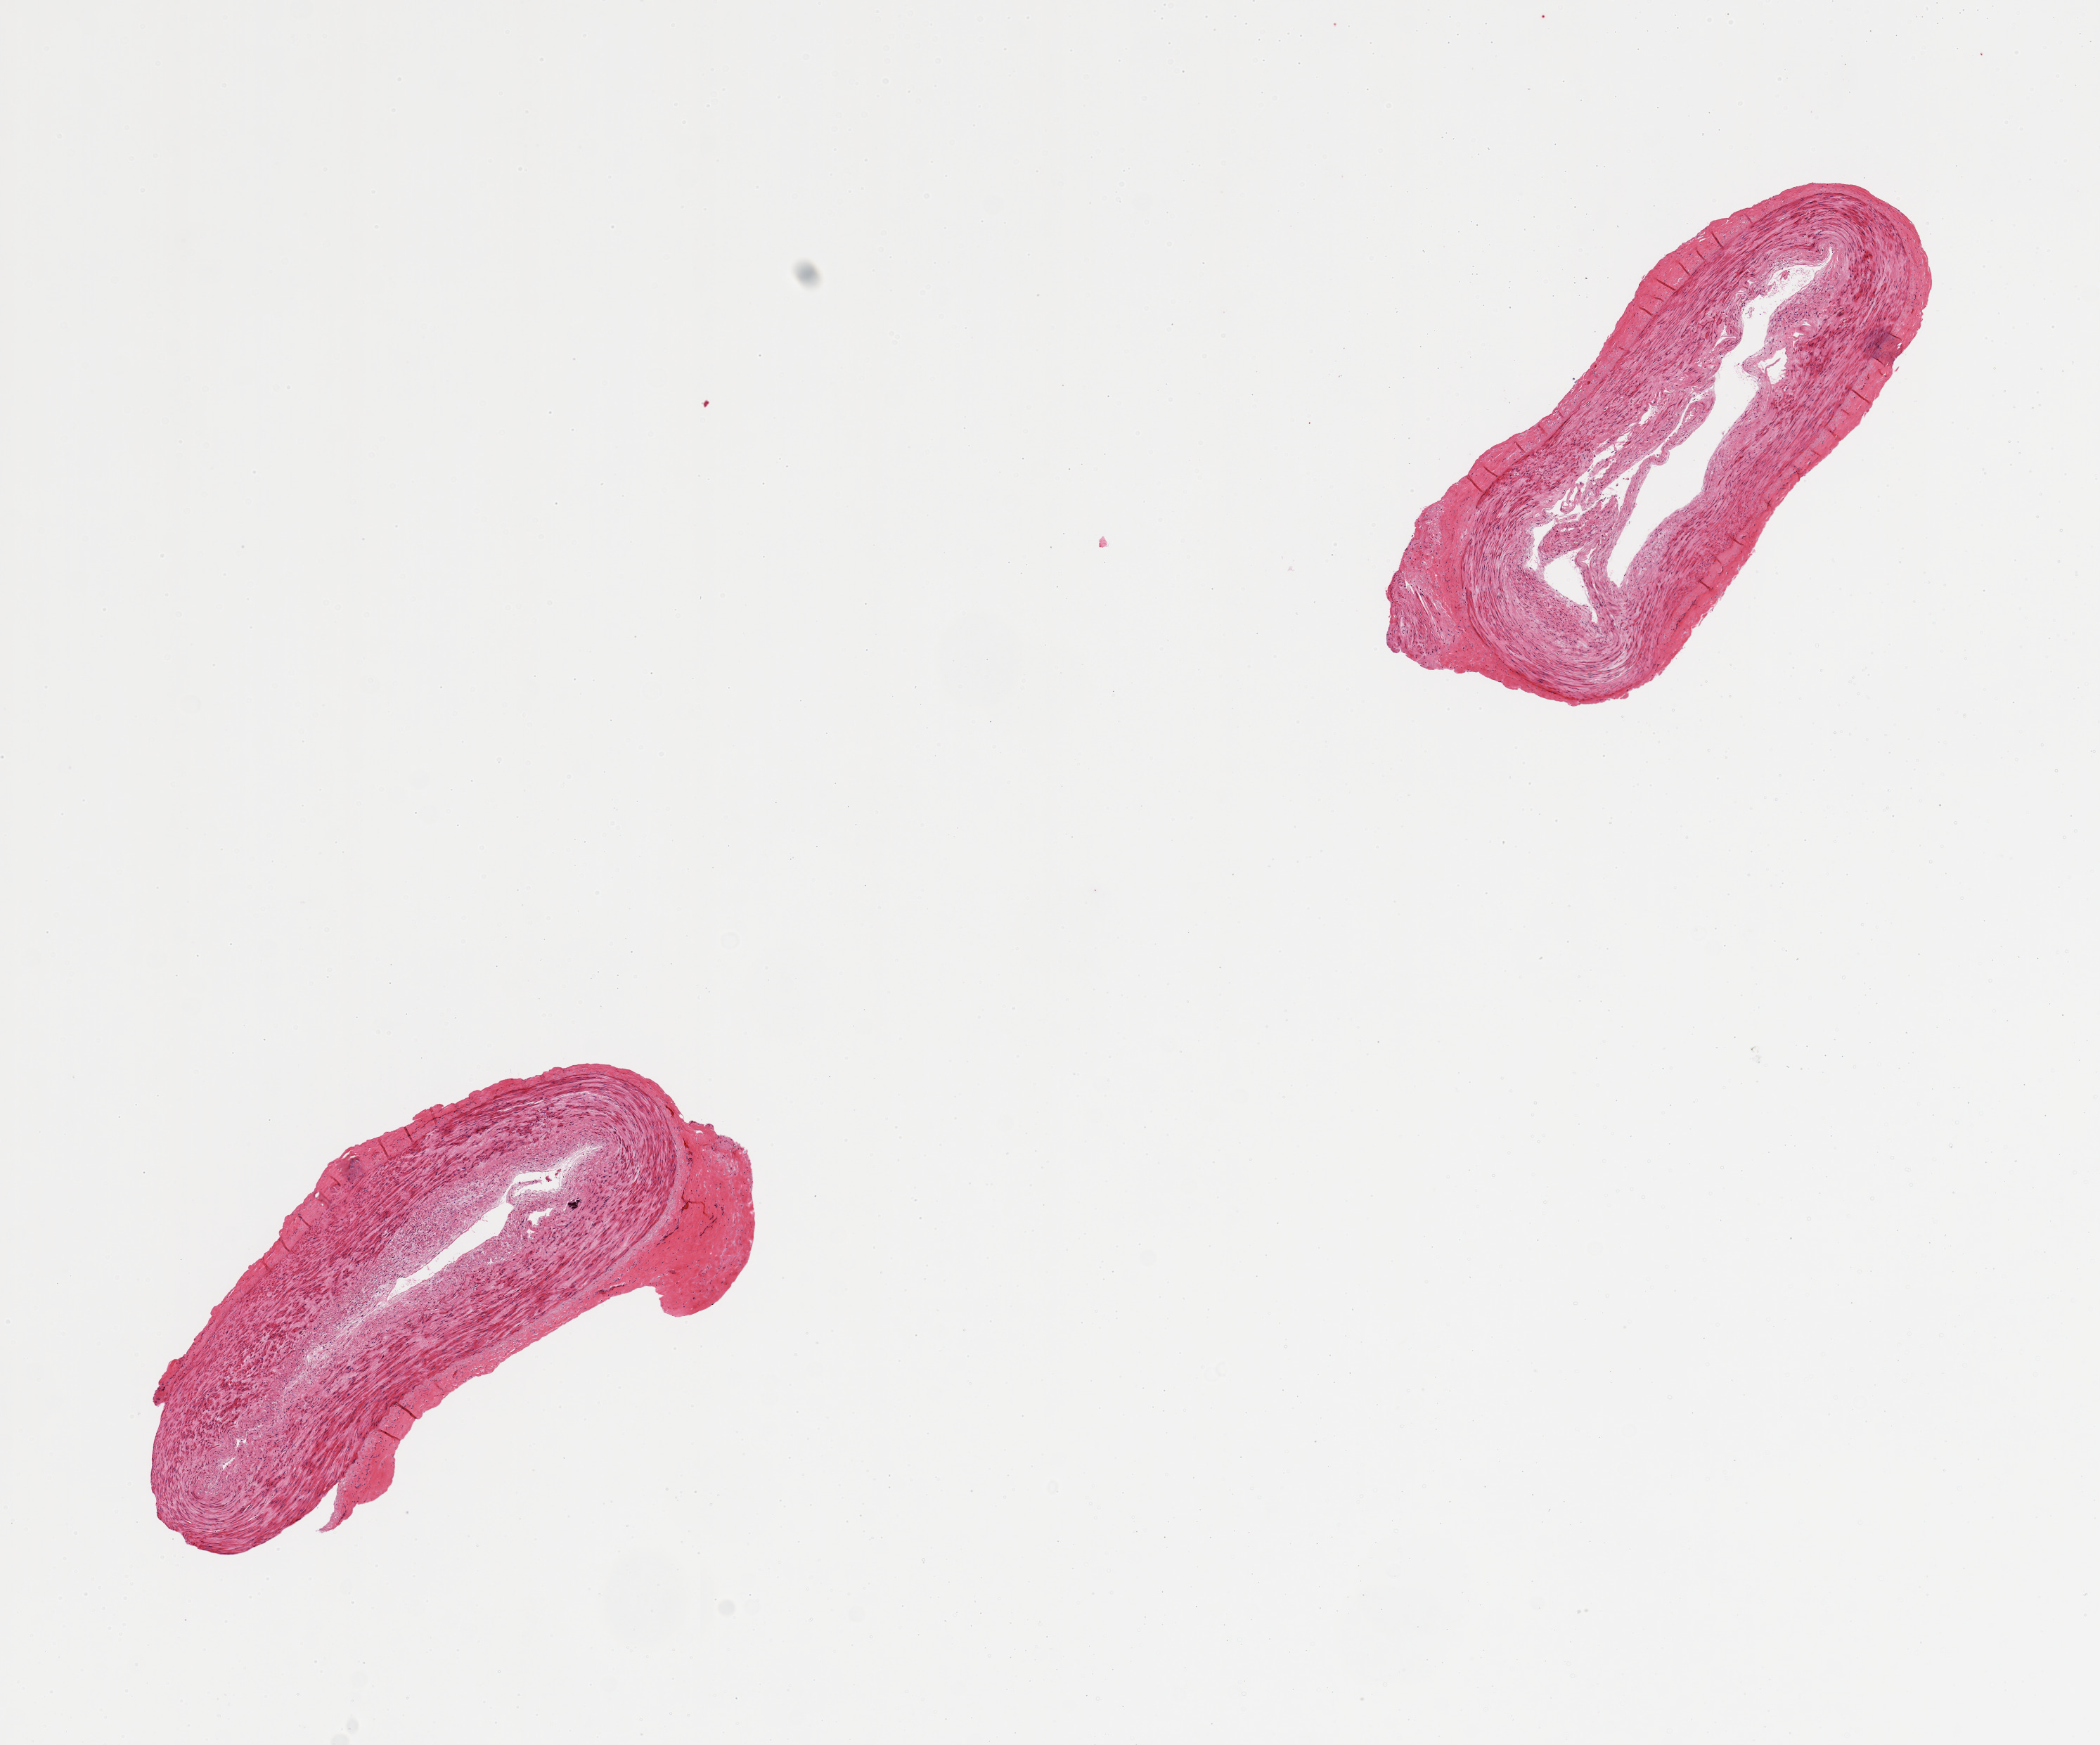
Whole-slide image, hematoxylin and eosin (H&E) stain — shown as a low-resolution overview of the whole scanned area (about 11.8 x 9.8 mm, acquisition: 20x scan). Male donor.
Specimen: PAXgene-fixed, paraffin-embedded tissue; sampled site (target tissue): tibial artery; donor tissue sample.